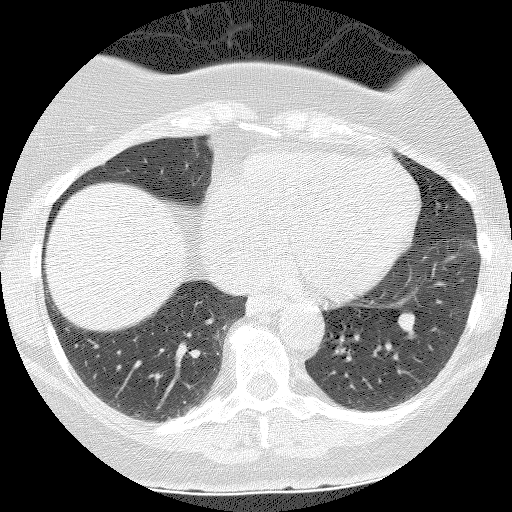
Low-dose screening chest CT, axial slice; second screening round (one year after baseline); lung window (W 1500 / L -600 HU); lung (sharp) reconstruction kernel (BONE); slice 93 of 140 in the series. Female participant, aged 55 years at enrolment. Former smoker at enrolment.
Lesion marked by an expert reader, bounding box [x1, y1, x2, y2] px = [382, 305, 427, 347]. The screening reader recorded 3 non-calcified nodules or masses ≥4 mm on this exam (left lower lobe, right lower lobe, right lower lobe); which of them this box marks is not recorded. Participant outcome: lung cancer diagnosed 655 days after this screen (after the third annual screen) — carcinoid tumor, NOS, left lower lobe, carcinoid, stage not assessed, 10 mm at pathology.